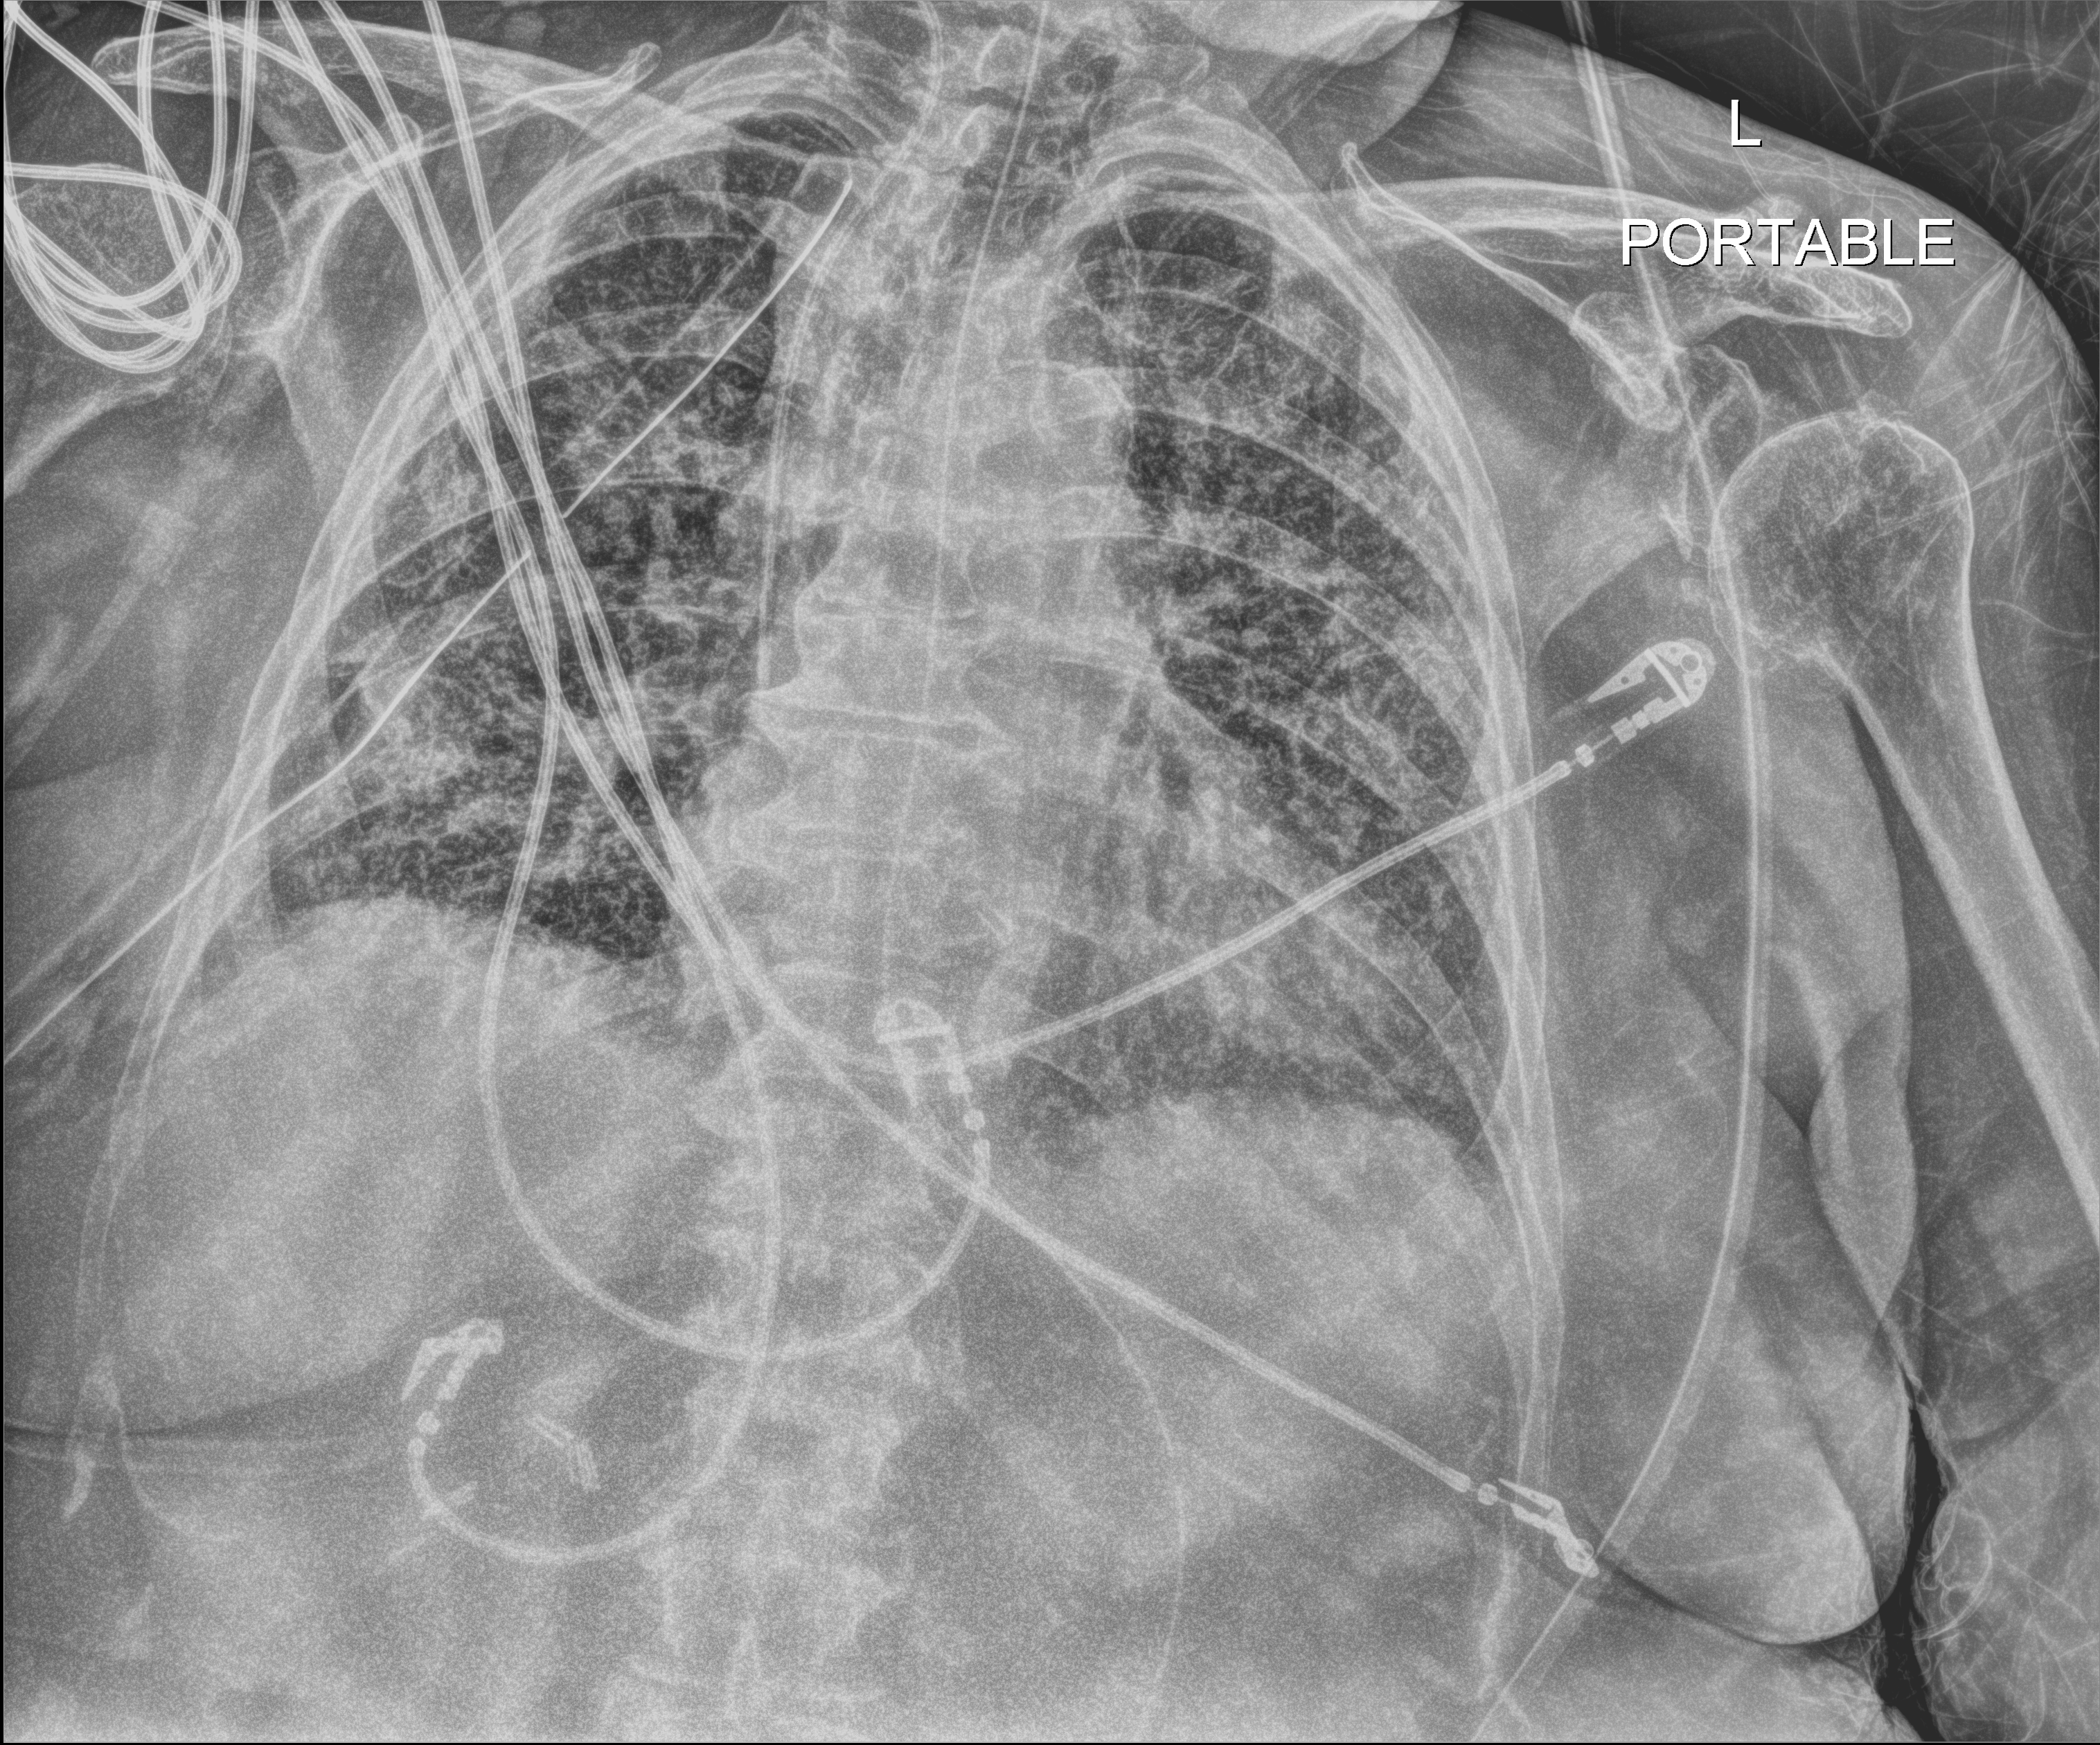
Bedside chest radiograph (digital radiography), anteroposterior (AP) projection. Female patient hospitalised with COVID-19, age 75–90 years.
From the hospital-stay record, not from the radiograph (when in the stay this image was taken is not recorded):
- length of hospital stay: 56 days
- chronic kidney disease (admission record): no
- admitted to intensive care during this hospital stay: no